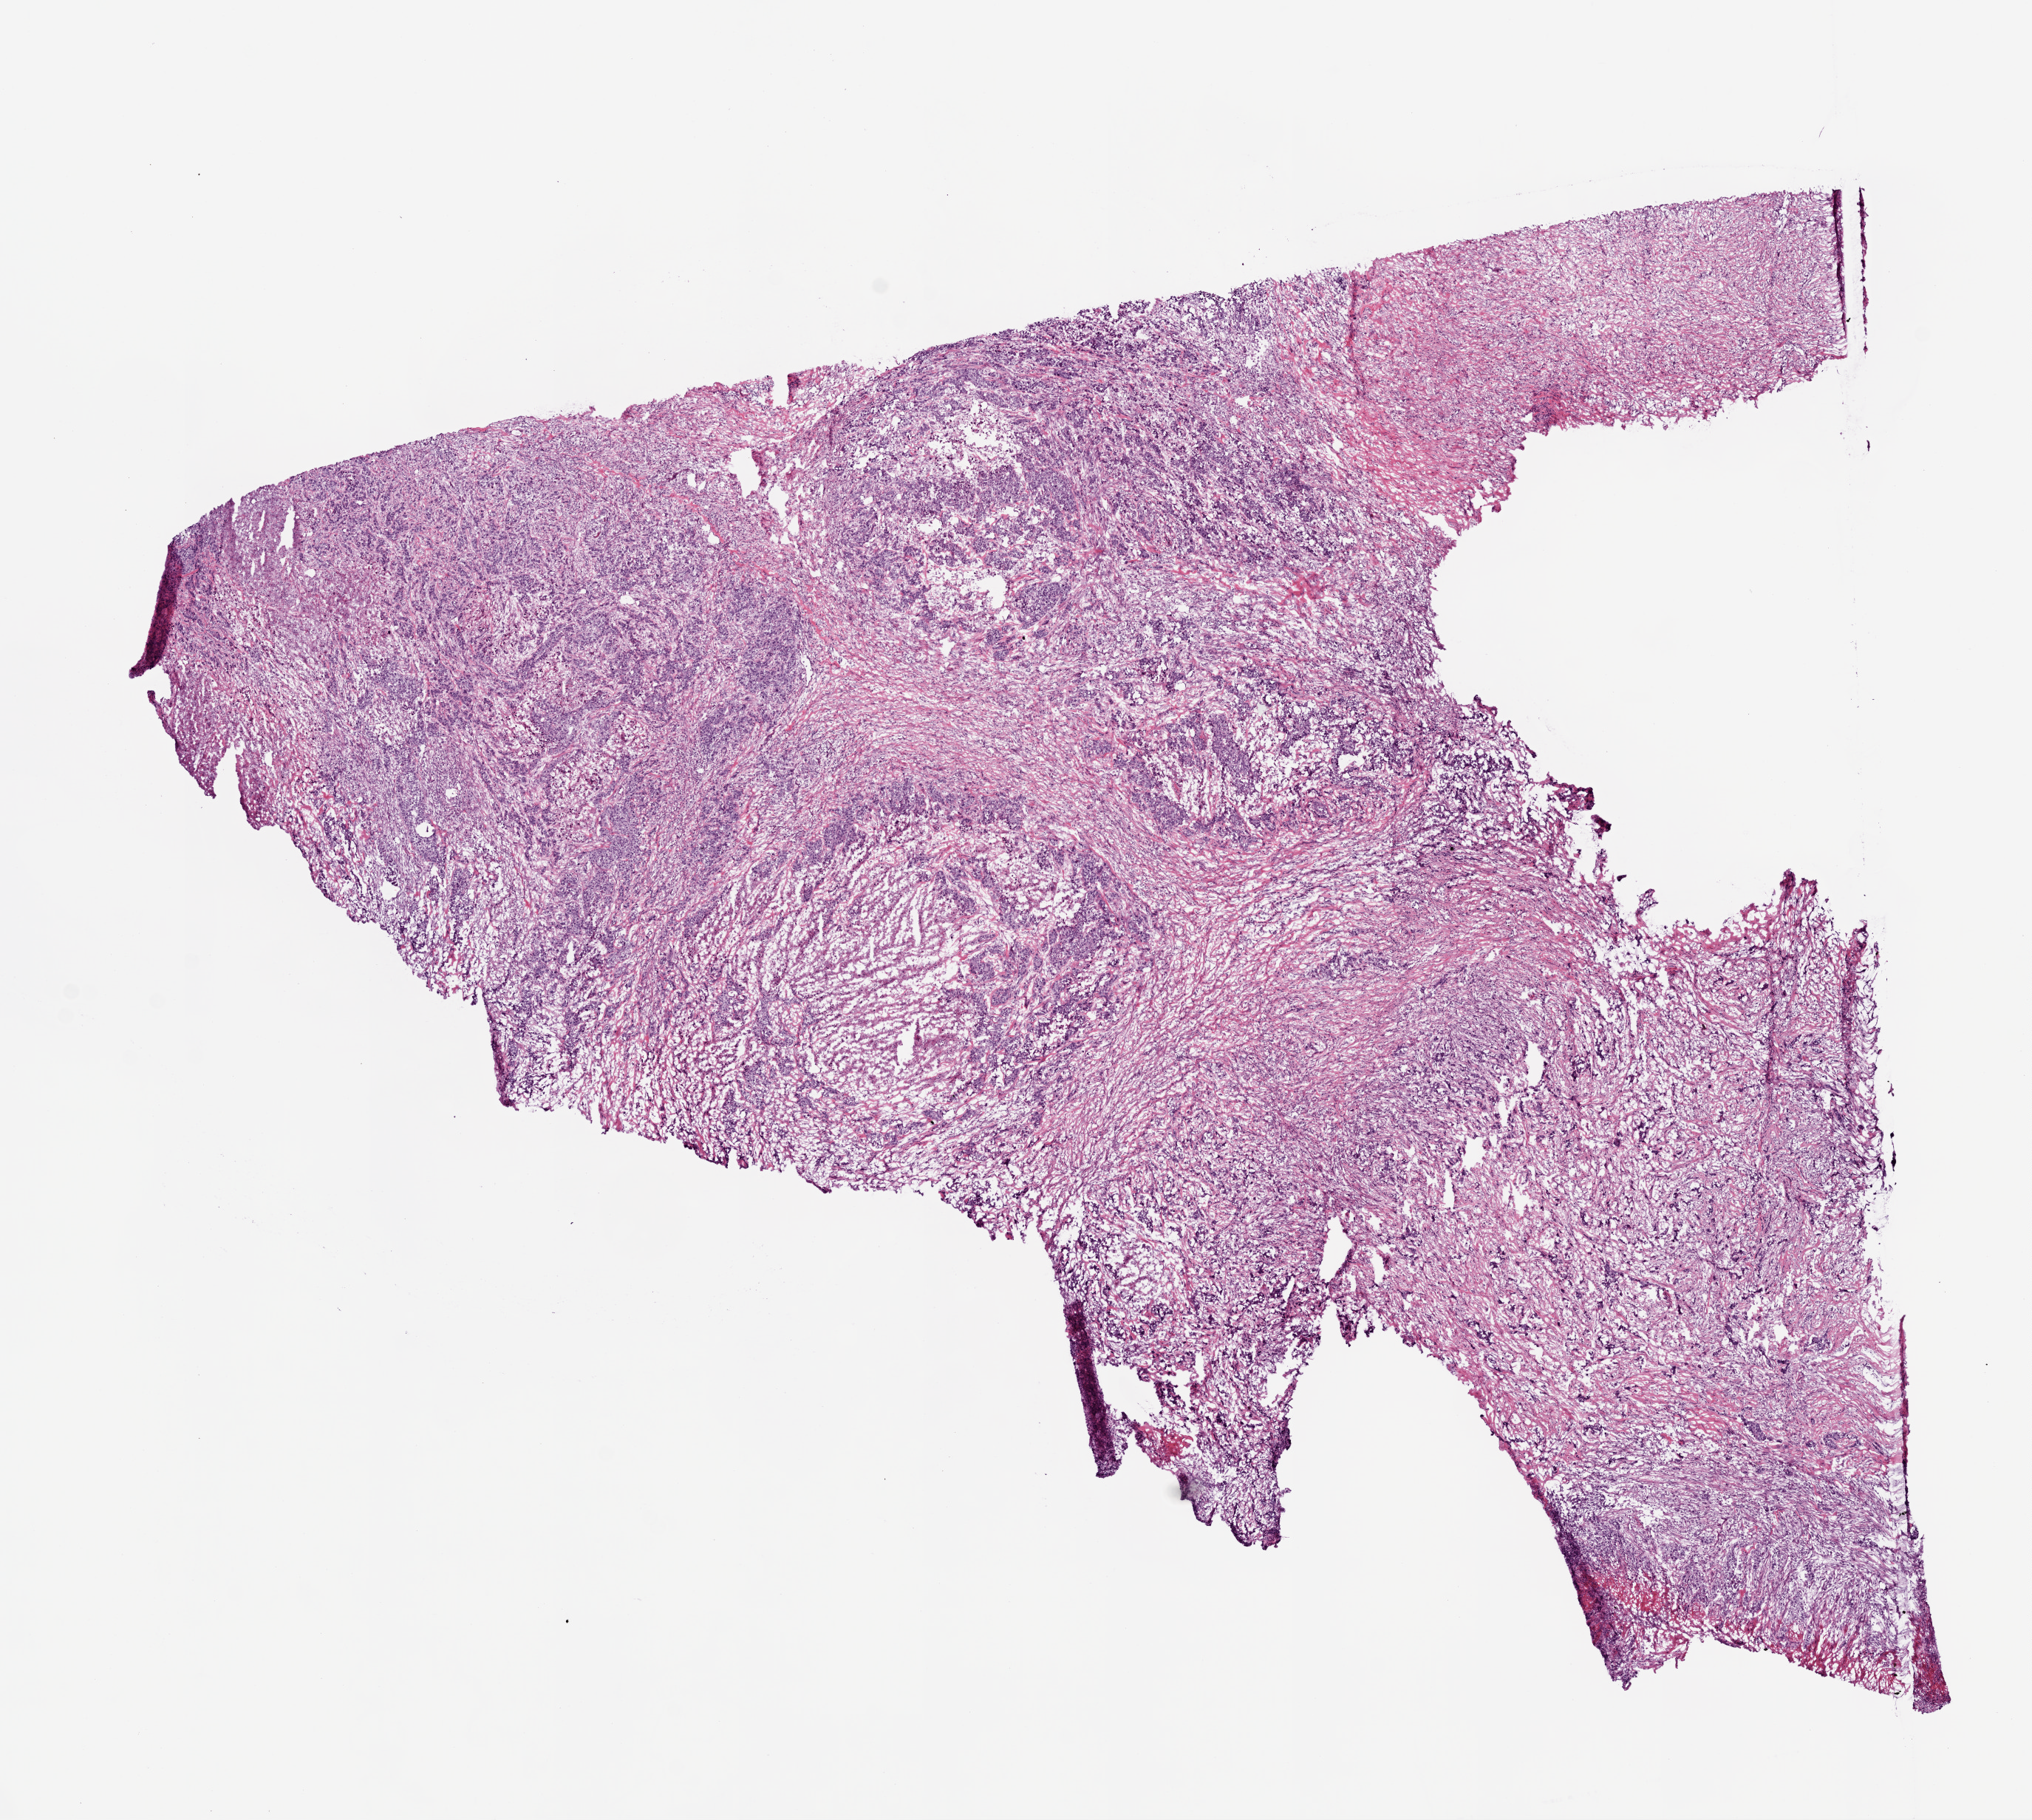
Whole-slide histology image, H&E-stained, shown as a low-resolution overview of the whole scanned area (about 11.0 x 9.9 mm, slide scanned at 20x), frozen section from the top of the tissue portion, stomach, primary tumour sample. Male patient; age at initial diagnosis 59 years. Histologic grade: G3 (poorly differentiated). Pathologist review of this section (percent, as recorded): tumour cells 52%, tumour nuclei 75%, normal cells 0%, stromal cells 30%, necrosis 18%.
Histologic diagnosis: Carcinoma, diffuse type (gastric antrum). Lymph nodes positive (case pathology): 34 of 40 examined. TNM: T3 N3 M1. AJCC pathologic stage: IV.